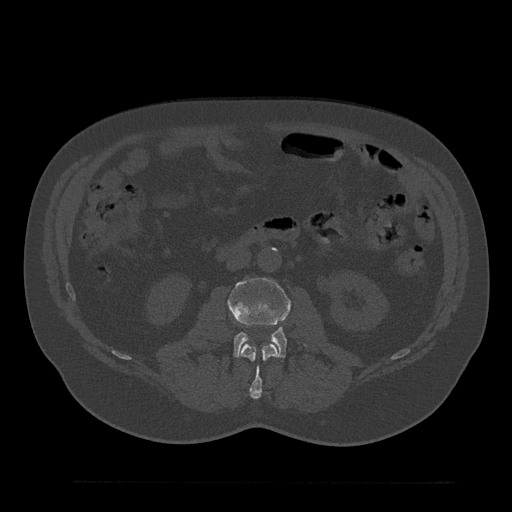
CT including the spine, one axial slice; slice 63 of 797 in the series (ordered by position); reconstruction kernel Br40s/3; bone window (W 1800 / L 400 HU); 0.5 mm slice thickness; 512 × 512 image matrix. Patient: male, 61 years. From the clinical record (not read from this slice): primary cancer: prostate.
Structures marked on this image (semi-automatically segmented with operator editing):
- L2 vertebra: bounding box <241,344,278,399> (left, top, right, bottom; pixels)
- L3 vertebra: <228,277,292,358>